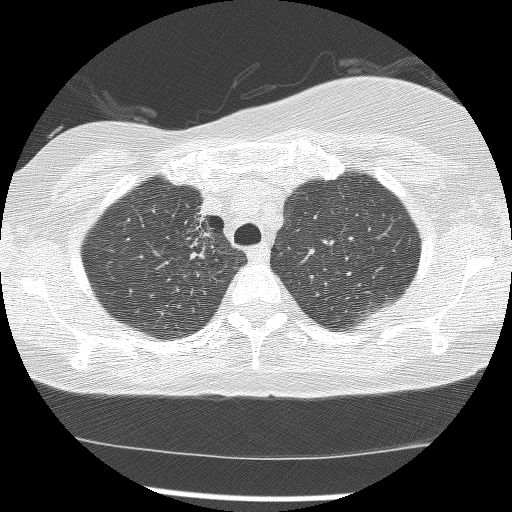
Chest CT (low-dose screening protocol), one axial image; baseline screening round; lung window (W 1500 / L -600 HU); 2.5 mm slice thickness; slice 34 of 172 in the series. Female, age 56 years at enrolment. Current smoker at enrolment.
Expert reader's lesion annotation, bounding box <166,204,225,276> (left, top, right, bottom; pixels). The screening reader recorded 2 non-calcified nodules or masses ≥4 mm on this exam (right lower lobe, right middle lobe); which of them this box marks is not recorded. Official screen result: positive, change unspecified: nodule(s) >= 4 mm or enlarging nodule(s), mass(es), or other non-specific abnormalities suspicious for lung cancer. Later outcome: lung cancer diagnosed 1185 days after this screen — adenocarcinoma, NOS, right upper lobe, stage IIIB (AJCC 6th edition), 8 mm at pathology.